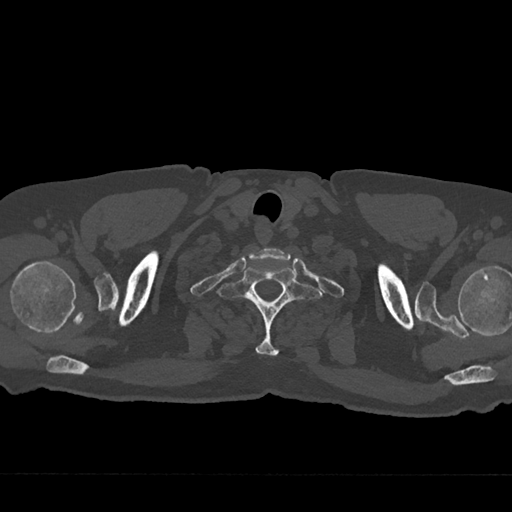
CT including the spine, one axial slice. Position 663 of 797 along the scan axis. 120 kVp. Bone window (W 1800 / L 400 HU). 0.5 mm slice thickness. 512 × 512 image matrix. Male patient, age 75 years. Case-level facts recorded for this patient, not image findings: primary cancer: renal; vertebrae with lytic lesions (as recorded): T4.
Outlined on this slice (semi-automatically segmented with operator editing):
- T1 vertebra: bounding box <216,266,322,356> (left, top, right, bottom; pixels)
- T2 vertebra: <280,292,283,295>